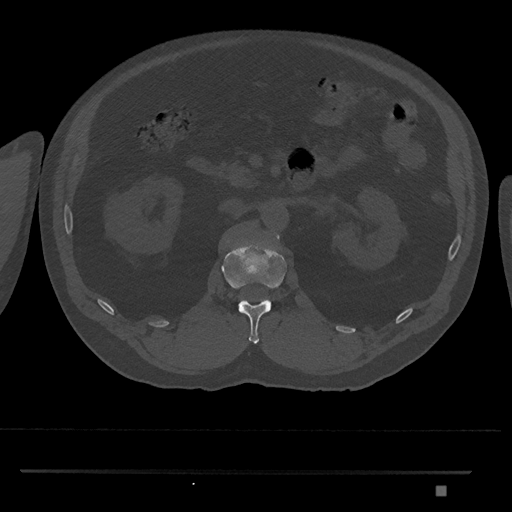
CT including the spine, one axial slice. Position 807 of 1134 along the scan axis. Reconstruction kernel Br40s/3. Bone window (W 1800 / L 400 HU). 0.5 mm slice thickness. 512 × 512 image matrix. Patient: male, 65 years. Case-level facts recorded for this patient, not image findings: primary cancer: prostate.
Structures marked on this image (semi-automatically segmented with operator editing):
- L1 vertebra: bounding box (x1, y1, x2, y2) in pixels: (222, 231, 287, 344)